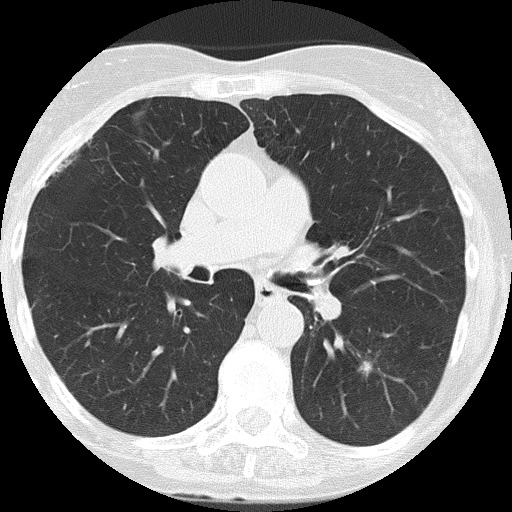
Low-dose screening chest CT, axial slice. Second annual screen. Lung window (W 1500 / L -600 HU). 2 mm slice thickness. Lung (sharp) reconstruction kernel (FC51). Slice 70 of 159 in the series. Female, age 68 years at enrolment. Former smoker at enrolment.
Lesion marked by an expert reader, bounding box <342,343,392,391> (left, top, right, bottom; pixels). Screening reader's record for this exam: no non-calcified nodule ≥4 mm recorded.